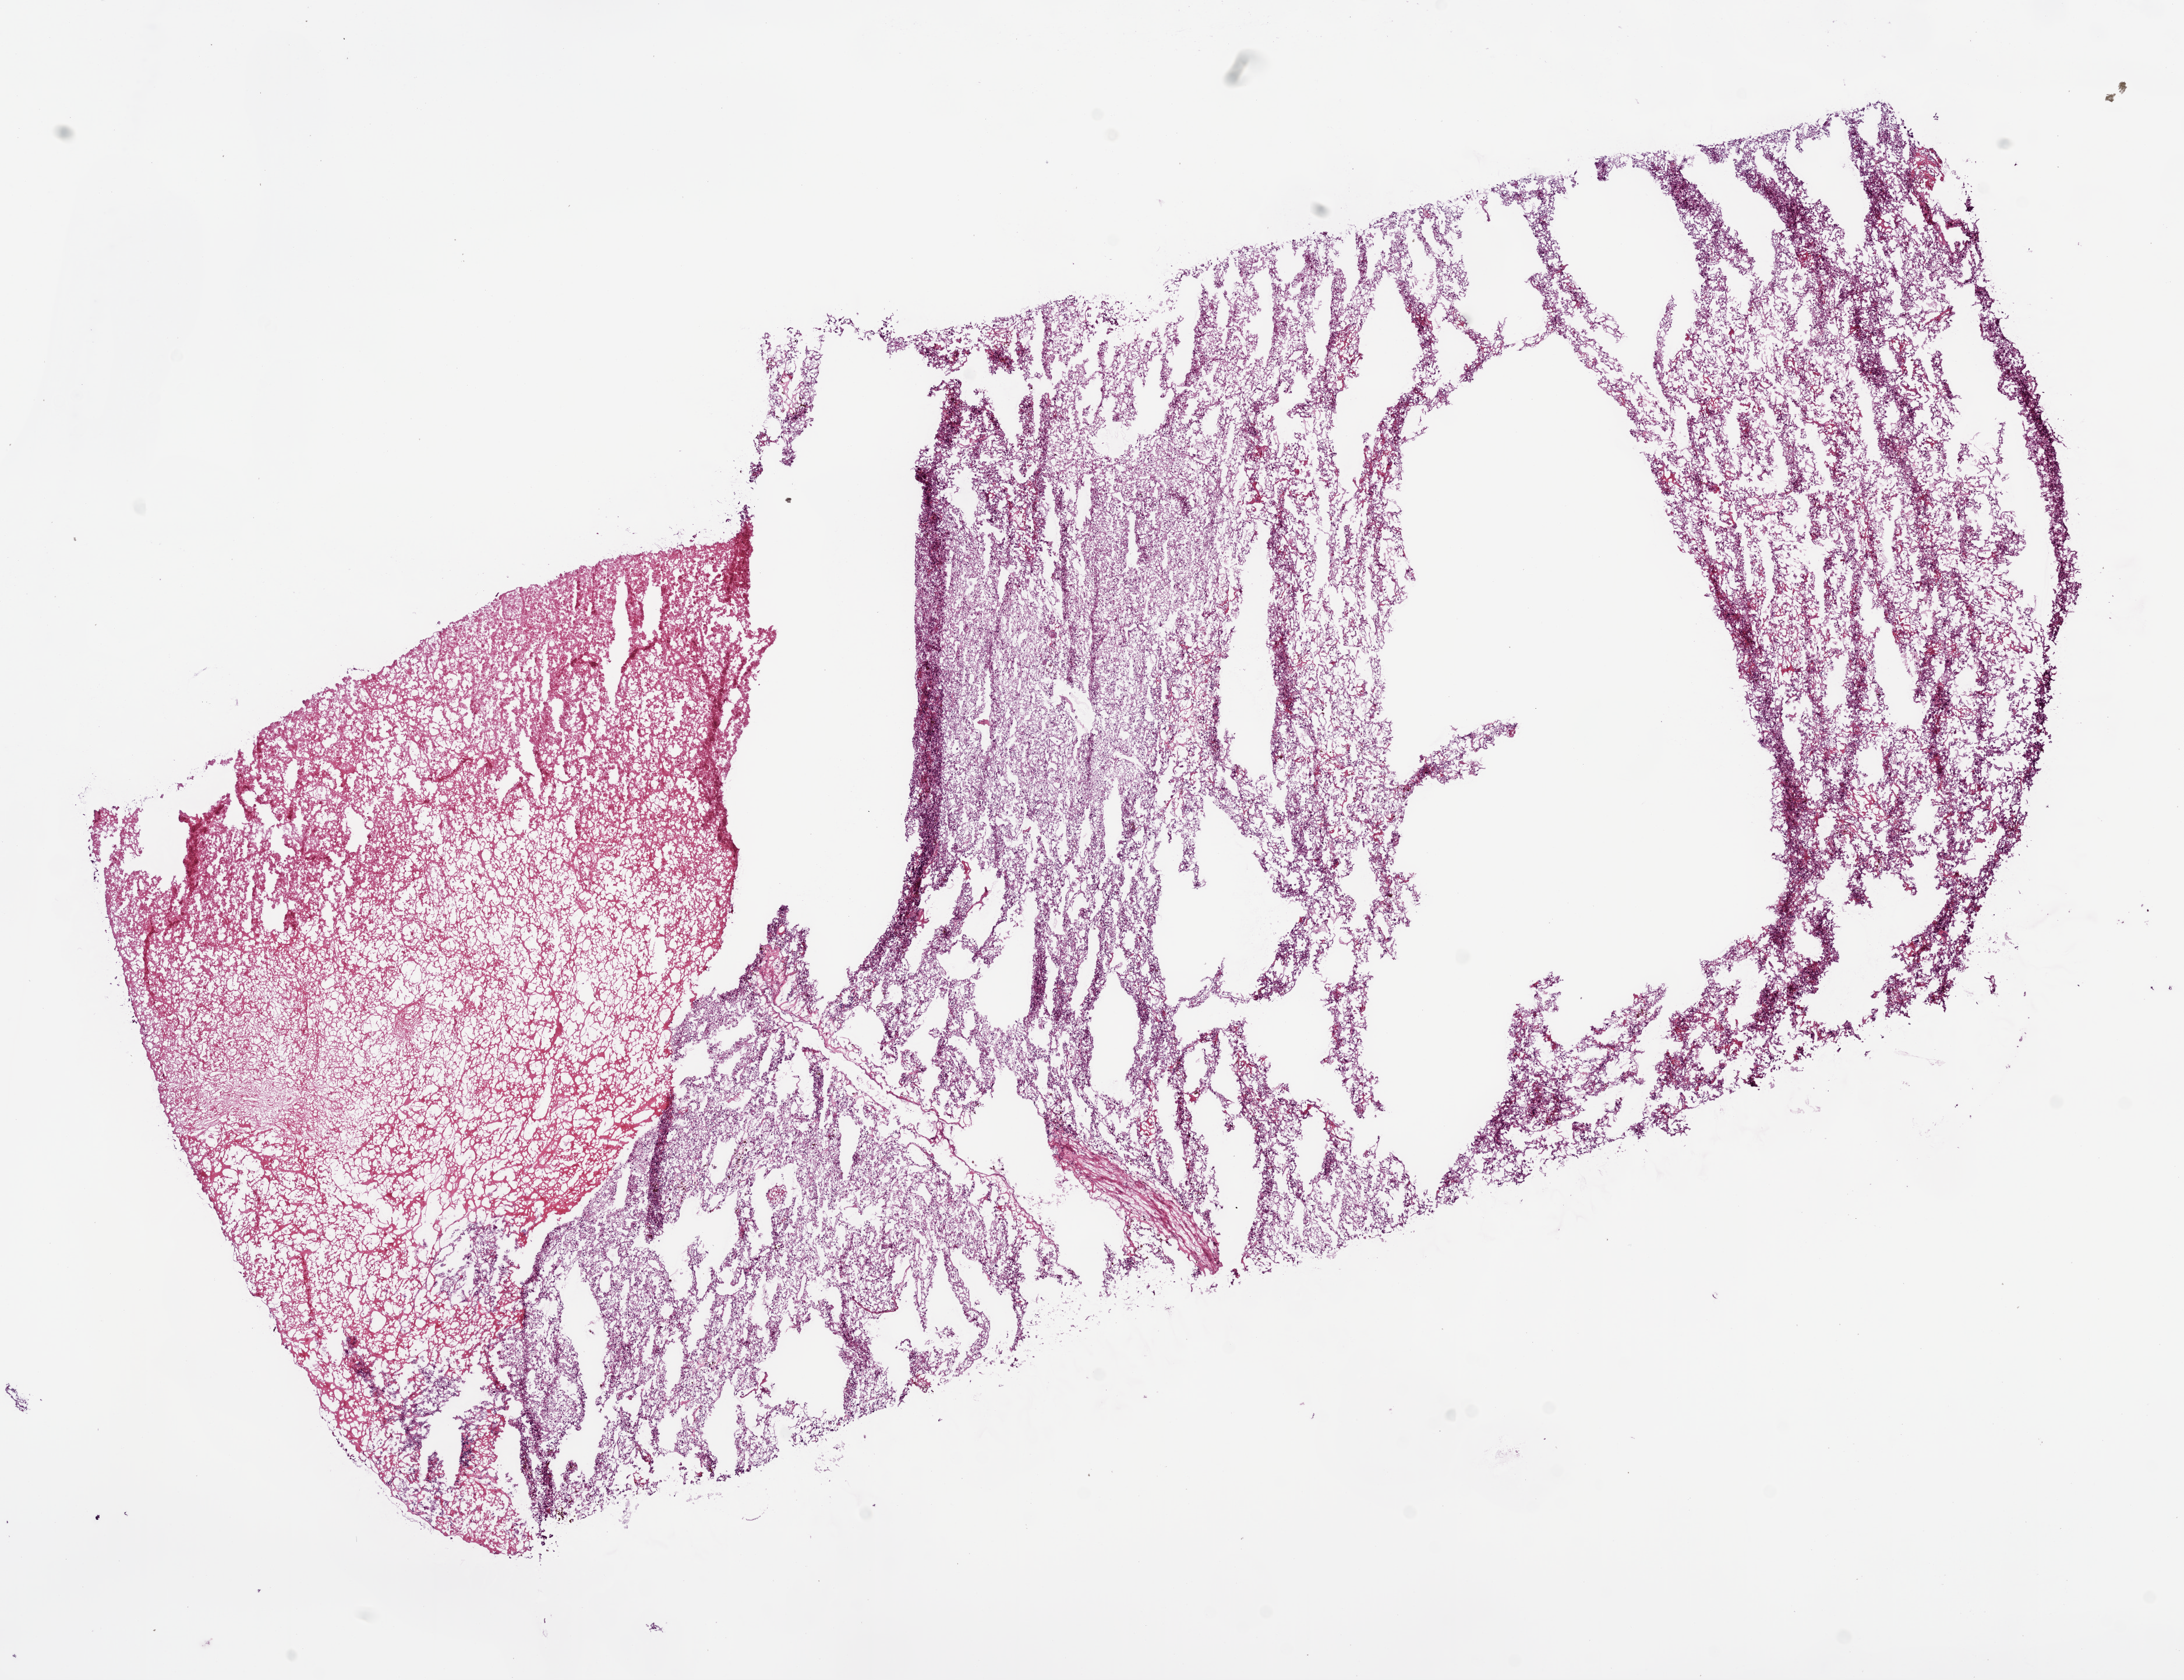
H&E whole-slide image — shown as a low-resolution overview of the whole scanned area (about 15.0 x 11.6 mm, slide scanned at 20x). Frozen section from the bottom of the tissue portion. Kidney, primary tumour sample. Patient: male, age at initial diagnosis 71 years. Histologic grade: G4 (undifferentiated). Slide review estimates, as recorded: tumour cells 65%, tumour nuclei 80%, normal cells 0%, stromal cells 5%, necrosis 30%.
Diagnosis: Clear cell adenocarcinoma, NOS. AJCC pathologic stage: IV.